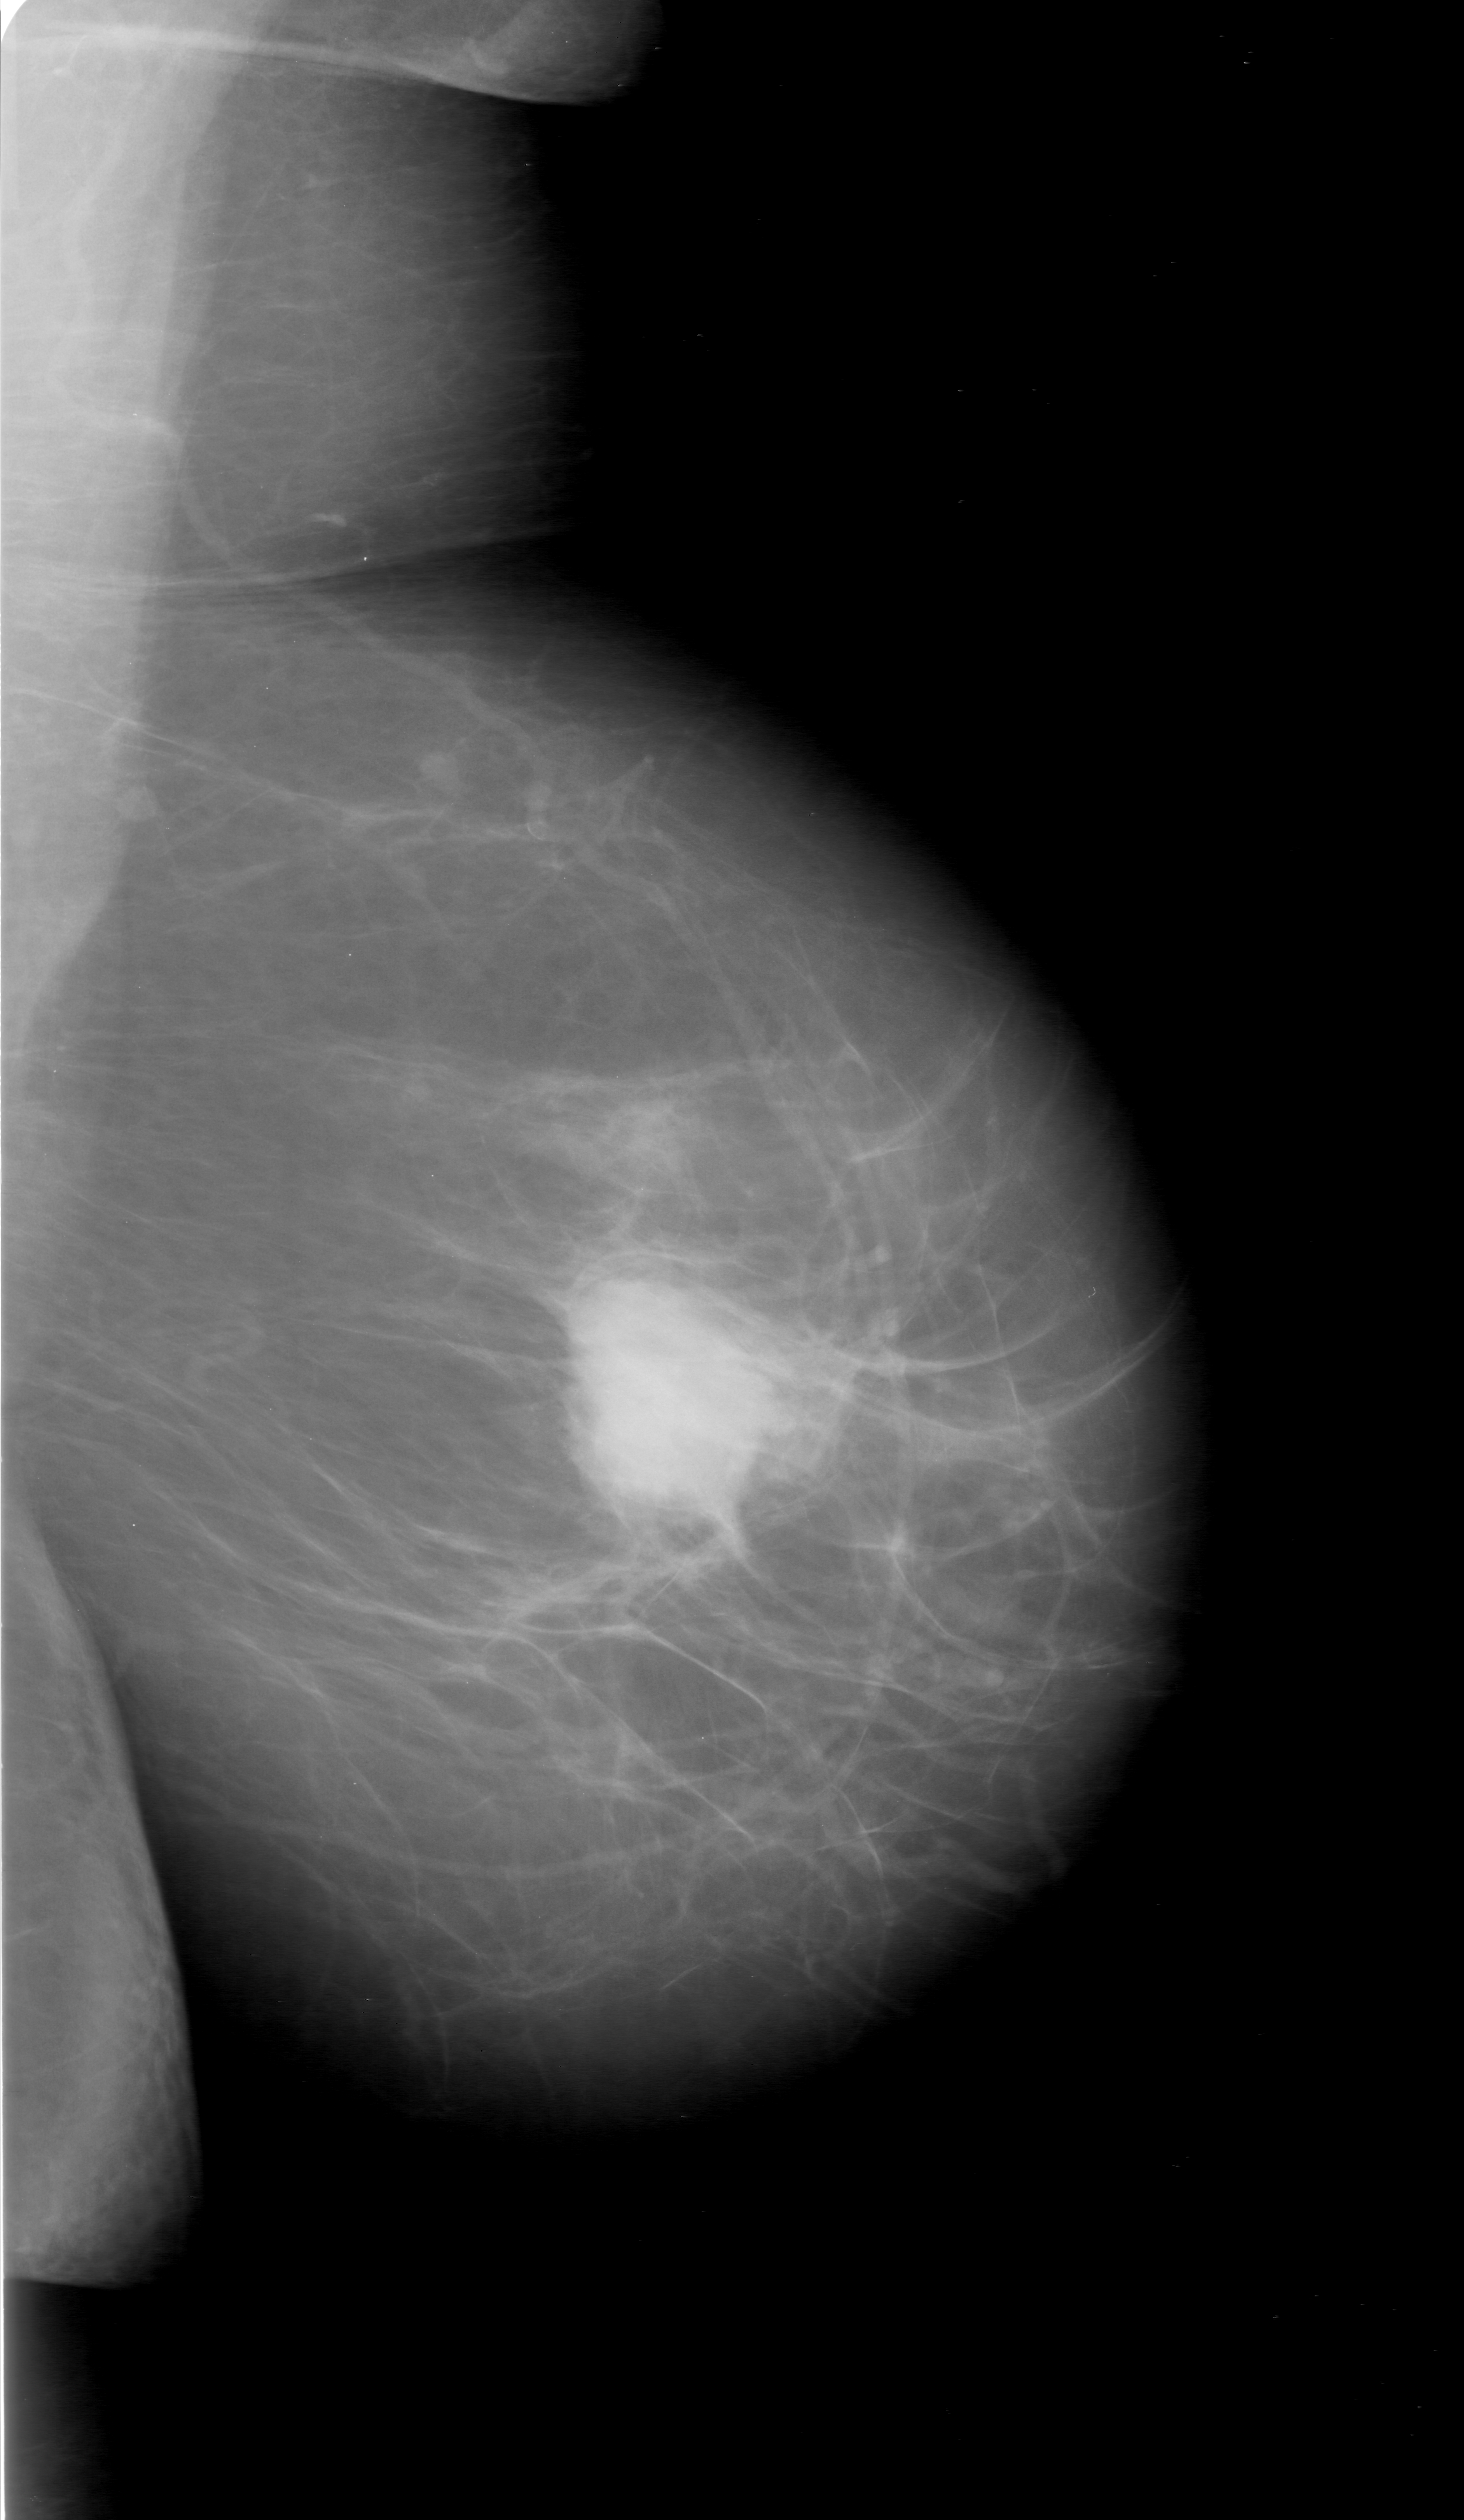
Scanned film-screen mammogram; left breast; MLO view; BI-RADS breast density category 2 (scale 1–4).
Abnormality record for this image: mass, shape oval, margins spiculated; BI-RADS assessment category 3; subtlety rating 5 on a 1 (subtle) to 5 (obvious) scale; pathology result (as recorded, not read from the image): malignant.